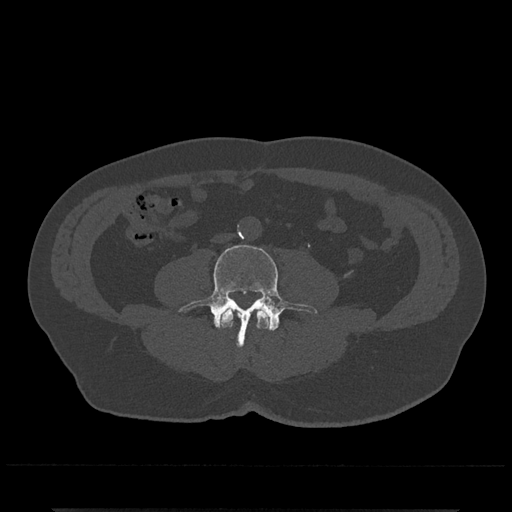
CT including the spine, one axial slice. Position 165 of 797 along the scan axis. 120 kVp. Bone window (W 1800 / L 400 HU). 512 × 512 image matrix, field of view 393 × 393 mm. Male patient, age 67 years. From the clinical record (not read from this slice): primary cancer: prostate.
Structures marked on this image (semi-automatically segmented with operator editing):
- L3 vertebra: box from (x=220, y=308) to (x=271, y=330) px
- L4 vertebra: (x=179, y=244)–(x=317, y=347)